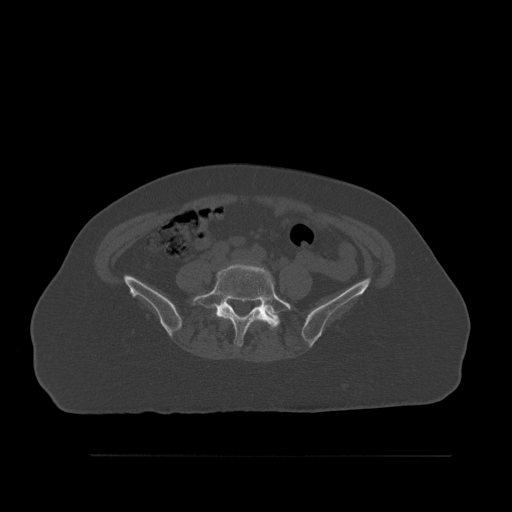
CT including the spine, one axial slice. Position 190 of 527 along the scan axis. Bone window (W 1800 / L 400 HU). 1.5 mm slice thickness. 512 × 512 image matrix, field of view 470 × 470 mm. Patient: female, 73 years. Case-level facts recorded for this patient, not image findings: primary cancer: breast.
Annotated regions visible in this slice (semi-automatically segmented with operator editing):
- L5 vertebra: bounding box (x1, y1, x2, y2) in pixels: (192, 264, 292, 347)